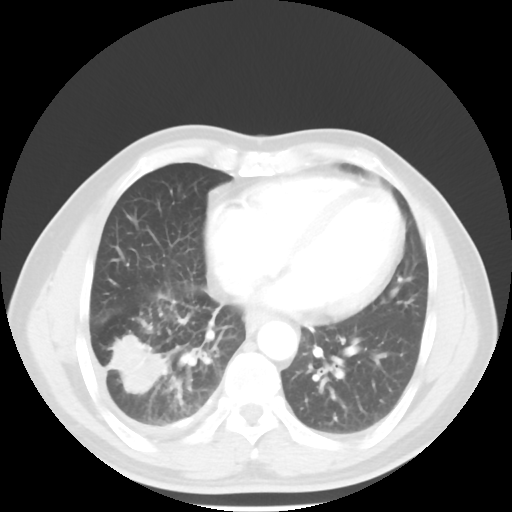
Chest CT, one axial slice. Slice 21 of 56 in the series (ordered by position). 120 kVp. Lung window (W 1500 / L -600 HU). 5 mm slice thickness. 512 × 512 image matrix. Patient: male, 56 years. From the clinical record (not read from this slice): clinical TNM (as recorded): T2 N3 M1.
Outlined on this slice (bounding box drawn by a radiologist):
- lung tumour (recorded histology: adenocarcinoma): bounding box <109,330,168,398> (left, top, right, bottom; pixels)